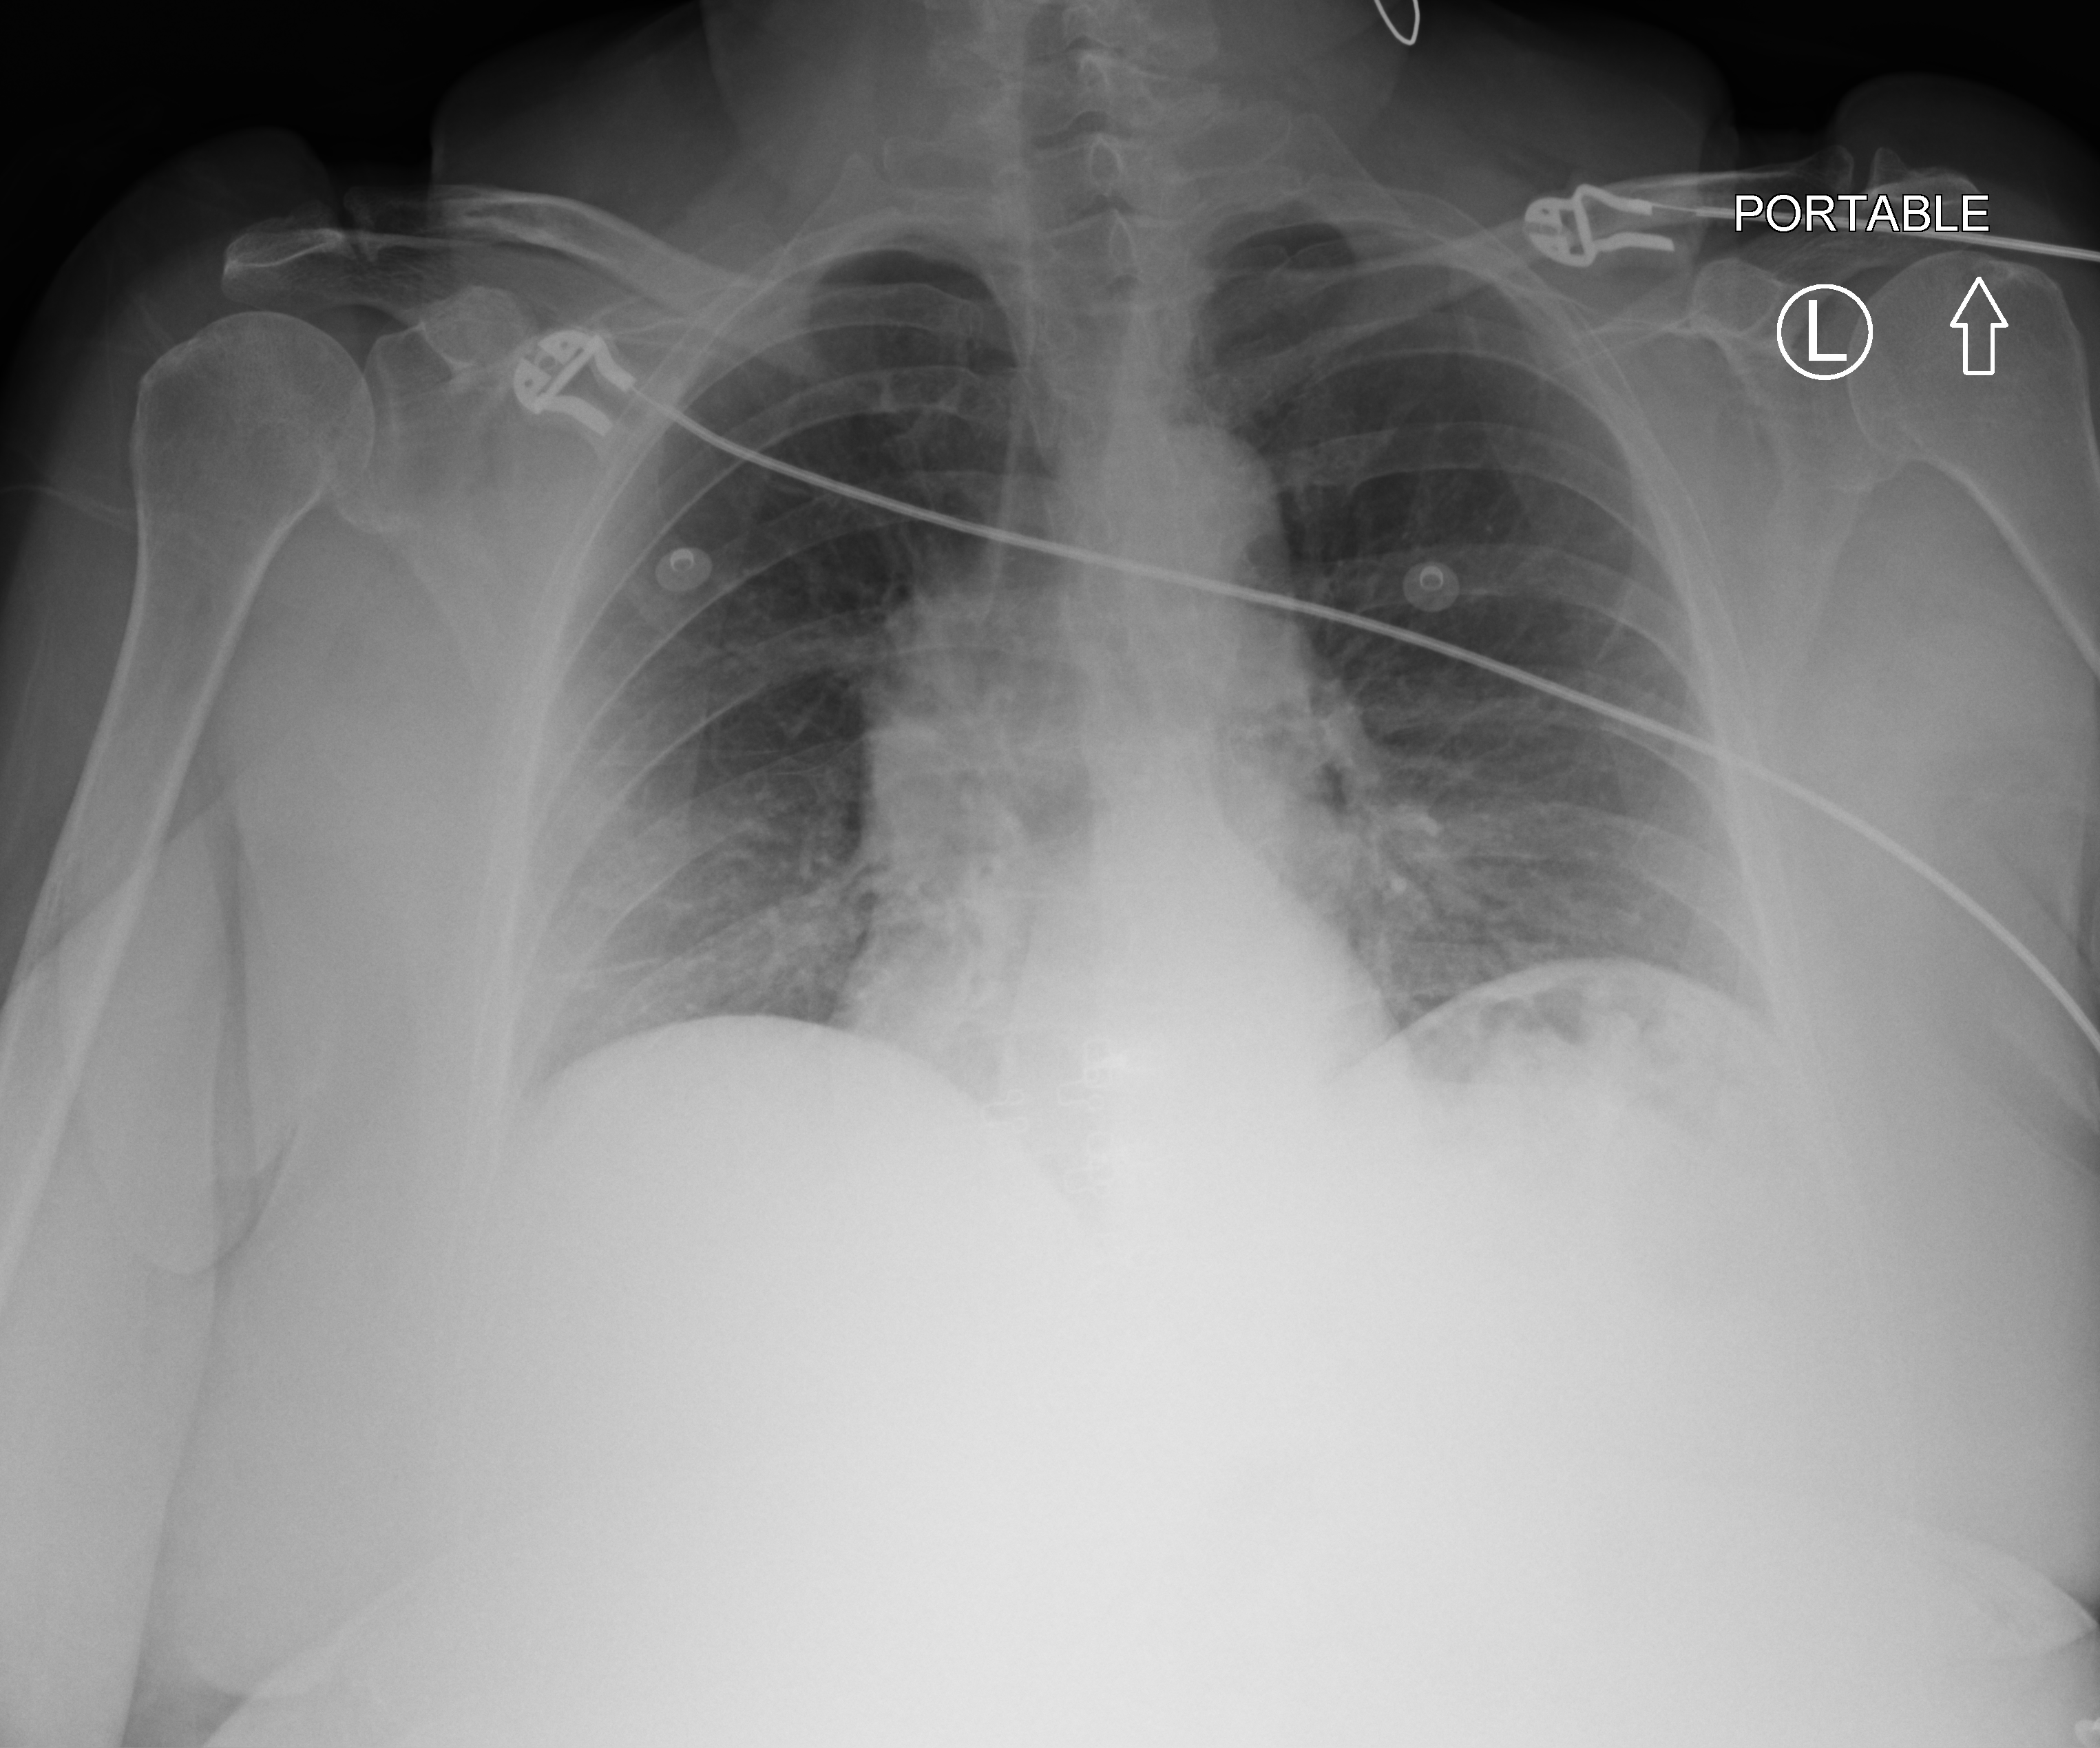
Chest X-ray (portable), anteroposterior (AP) projection. Patient hospitalised with COVID-19; female, aged 60–74 years.
Hospital-stay facts (about this admission, not read from this image; timing relative to this image not recorded):
- mechanically ventilated during this hospital stay: no
- admitted to intensive care during this hospital stay: no